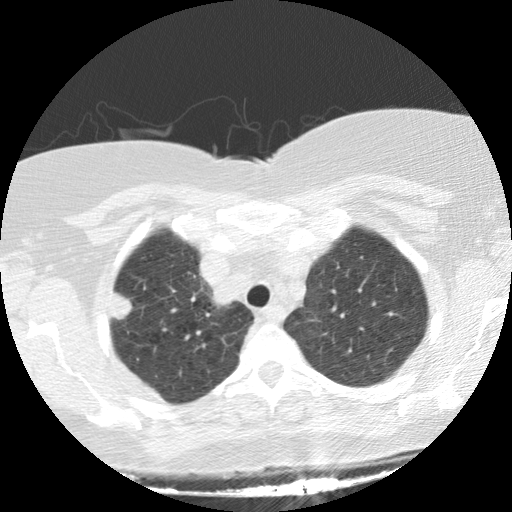
Axial slice from a low-dose chest CT screening exam; first (baseline) screen; lung window (W 1500 / L -600 HU); 512 × 512 image matrix. Female participant, aged 64 years at enrolment. Current smoker at enrolment.
Expert-annotated lung lesion, box from (x=97, y=279) to (x=145, y=331) px. Reader record for this screening exam (exam-level; its link to the box is not recorded): non-calcified nodule or mass ≥4 mm, right upper lobe, 17 × 16 mm, spiculated (stellate) margins, soft tissue attenuation. Official screen result: positive, change unspecified: nodule(s) >= 4 mm or enlarging nodule(s), mass(es), or other non-specific abnormalities suspicious for lung cancer.